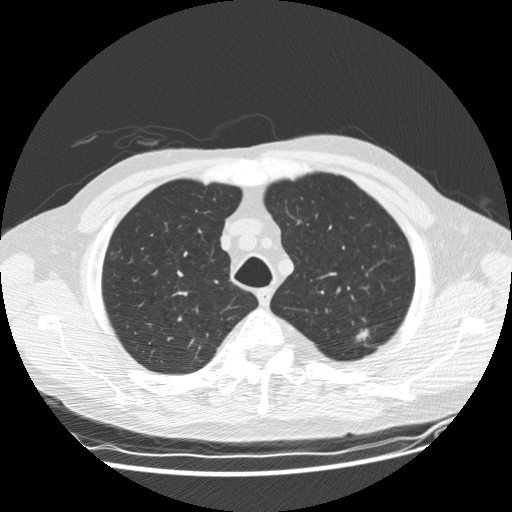
Low-dose screening chest CT, one axial slice; position 146 of 177 along the scan axis; reconstruction kernel STANDARD; 120 kVp; lung window (W 1500 / L -600 HU); 512 × 512 image matrix.
Structures marked on this image (outlined manually by an expert reader):
- lesion 1 (tumor, upper lobe of left lung): bounding box (x1, y1, x2, y2) in pixels: (356, 328, 369, 341)